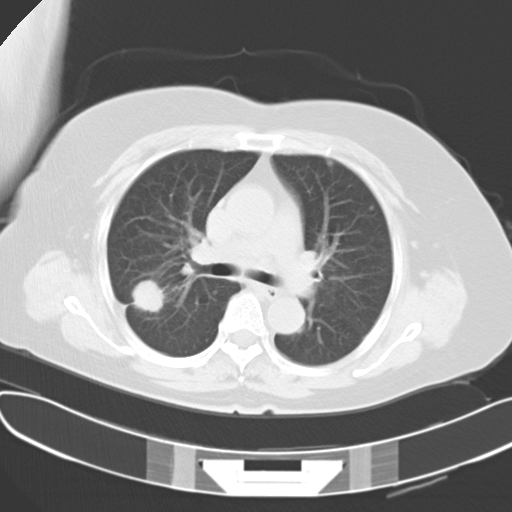
Chest CT, one axial slice; slice 22 of 30 in the series (ordered by position); reconstruction kernel B40f; lung window (W 1500 / L -600 HU); 10 mm slice thickness; 512 × 512 image matrix, field of view 367 × 367 mm. Patient: female, 63 years. From the clinical record (not read from this slice): clinical TNM (as recorded): T1c N3 M1a.
Outlined on this slice (bounding box drawn by a radiologist):
- lung tumour (recorded histology: adenocarcinoma): box from (x=126, y=268) to (x=166, y=320) px